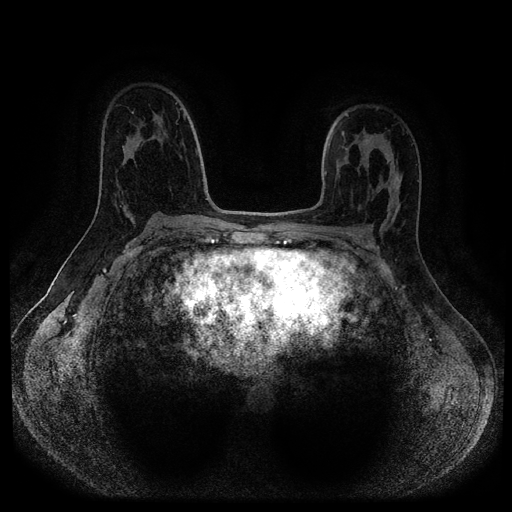
Breast MRI (dynamic contrast-enhanced, multi-phase), one axial slice. Dynamic contrast-enhanced series, time point 2 of 5 at this slice position (early post-contrast). 1.5 T. TE 2.7 ms, TR 5.4 ms. 2 mm slice thickness. 512 × 512 image matrix. Patient: female, 40 years.
Annotated regions visible in this slice (semi-automatically segmented with operator editing):
- breast lesion (labelled benign in the annotation): bounding box (x1, y1, x2, y2) in pixels: (121, 202, 136, 227)